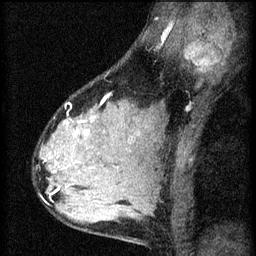
Breast MRI (dynamic contrast-enhanced), one sagittal slice. Slice 43 of 60 in the series (ordered by position). 3 images stored at this slice position (order not interpretable as contrast timing). 1.5 T. TE 4.2 ms, TR 8.2 ms. 2 mm slice thickness. 256 × 256 image matrix, field of view 180 × 180 mm. Patient: female, 37 years.
Structures marked on this image (semi-automatic segmentation, software-assisted and operator-edited):
- analysis volume of interest (the breast-tissue region the enhancement analysis was run in; not a lesion): bounding box [x1, y1, x2, y2] px = [44, 100, 119, 197]
- tumour enhancement mask (voxels above the 70 % enhancement threshold inside the analysis volume of interest): [53, 120, 89, 193]